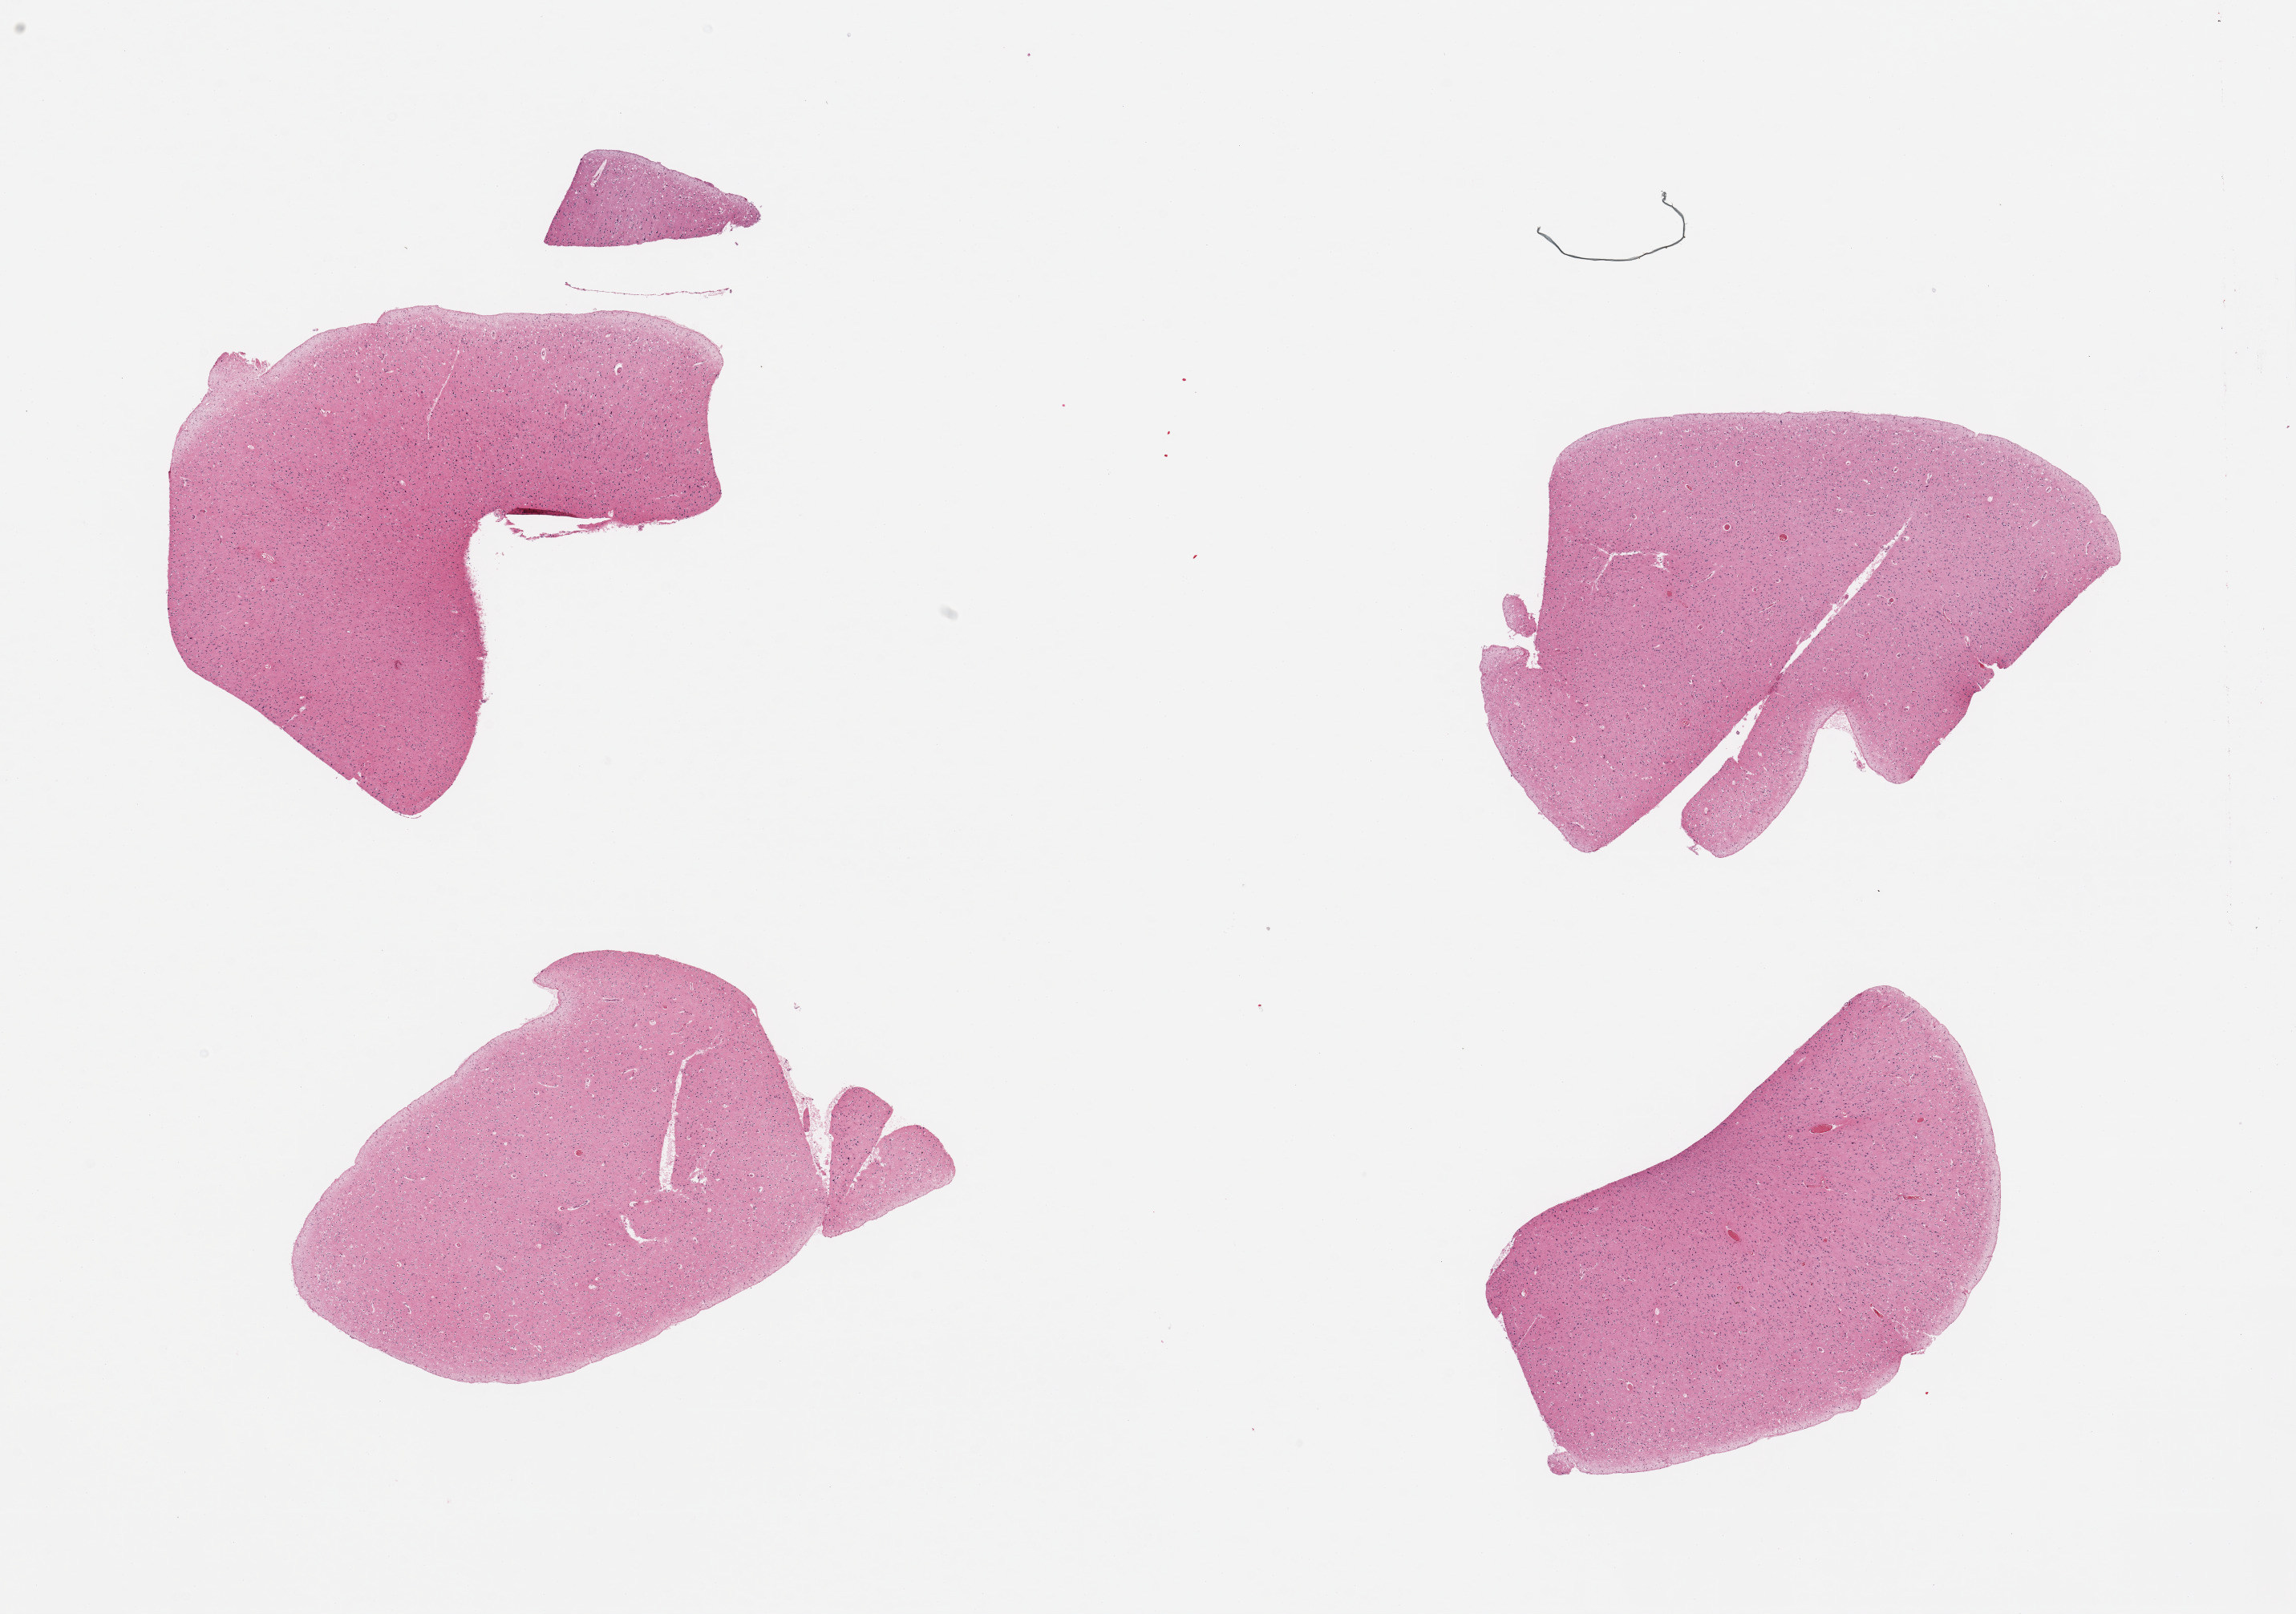
Digitized haematoxylin and eosin-stained section, brightfield — low-resolution overview of the scanned area, about 22.6 x 15.9 mm (slide scanned at 20x); PAXgene-fixed paraffin-embedded (PFPE) section; target tissue: cerebral cortex; donor tissue sample. Male donor.
Reviewer comment on this tissue sample: 4 pieces.